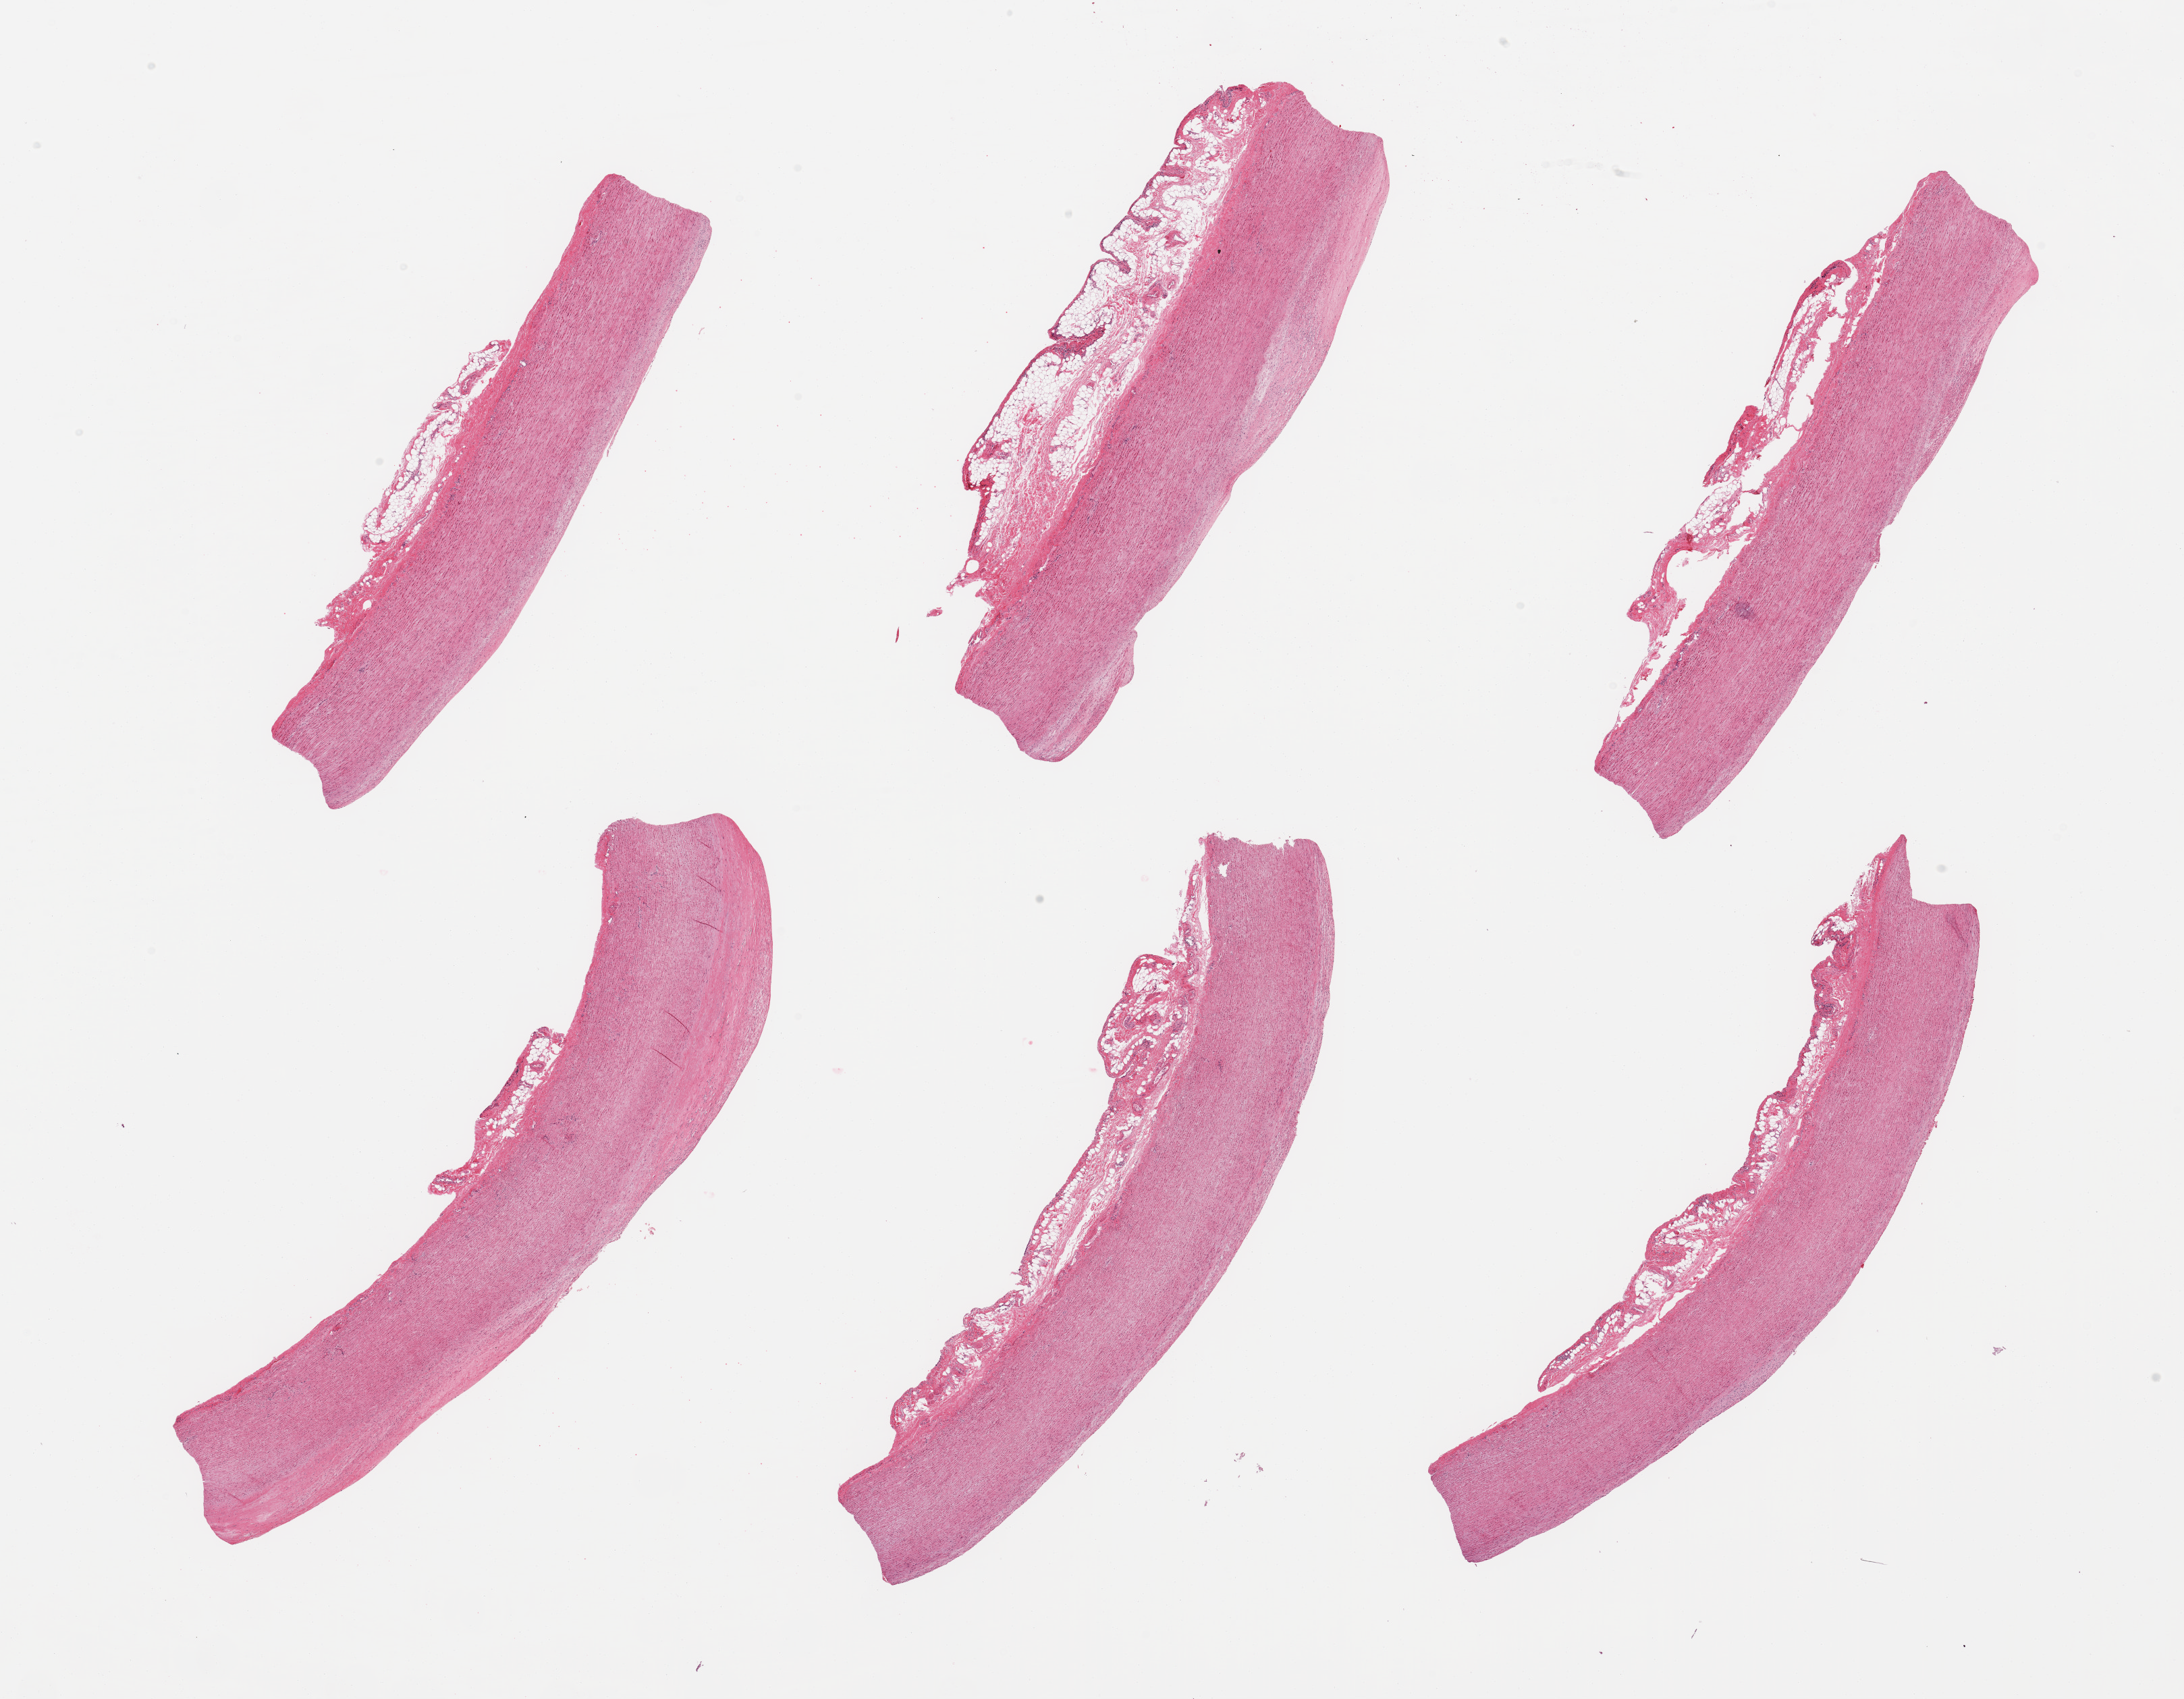
H&E whole-slide image — a low-resolution overview of the entire scanned area, about 25.6 x 19.9 mm; PAXgene-fixed paraffin-embedded (PFPE) section; target tissue: aorta; tissue donor sample. Donor sex: male.
Reviewer comment on this tissue sample: 6 pieces; atherosclerosis.